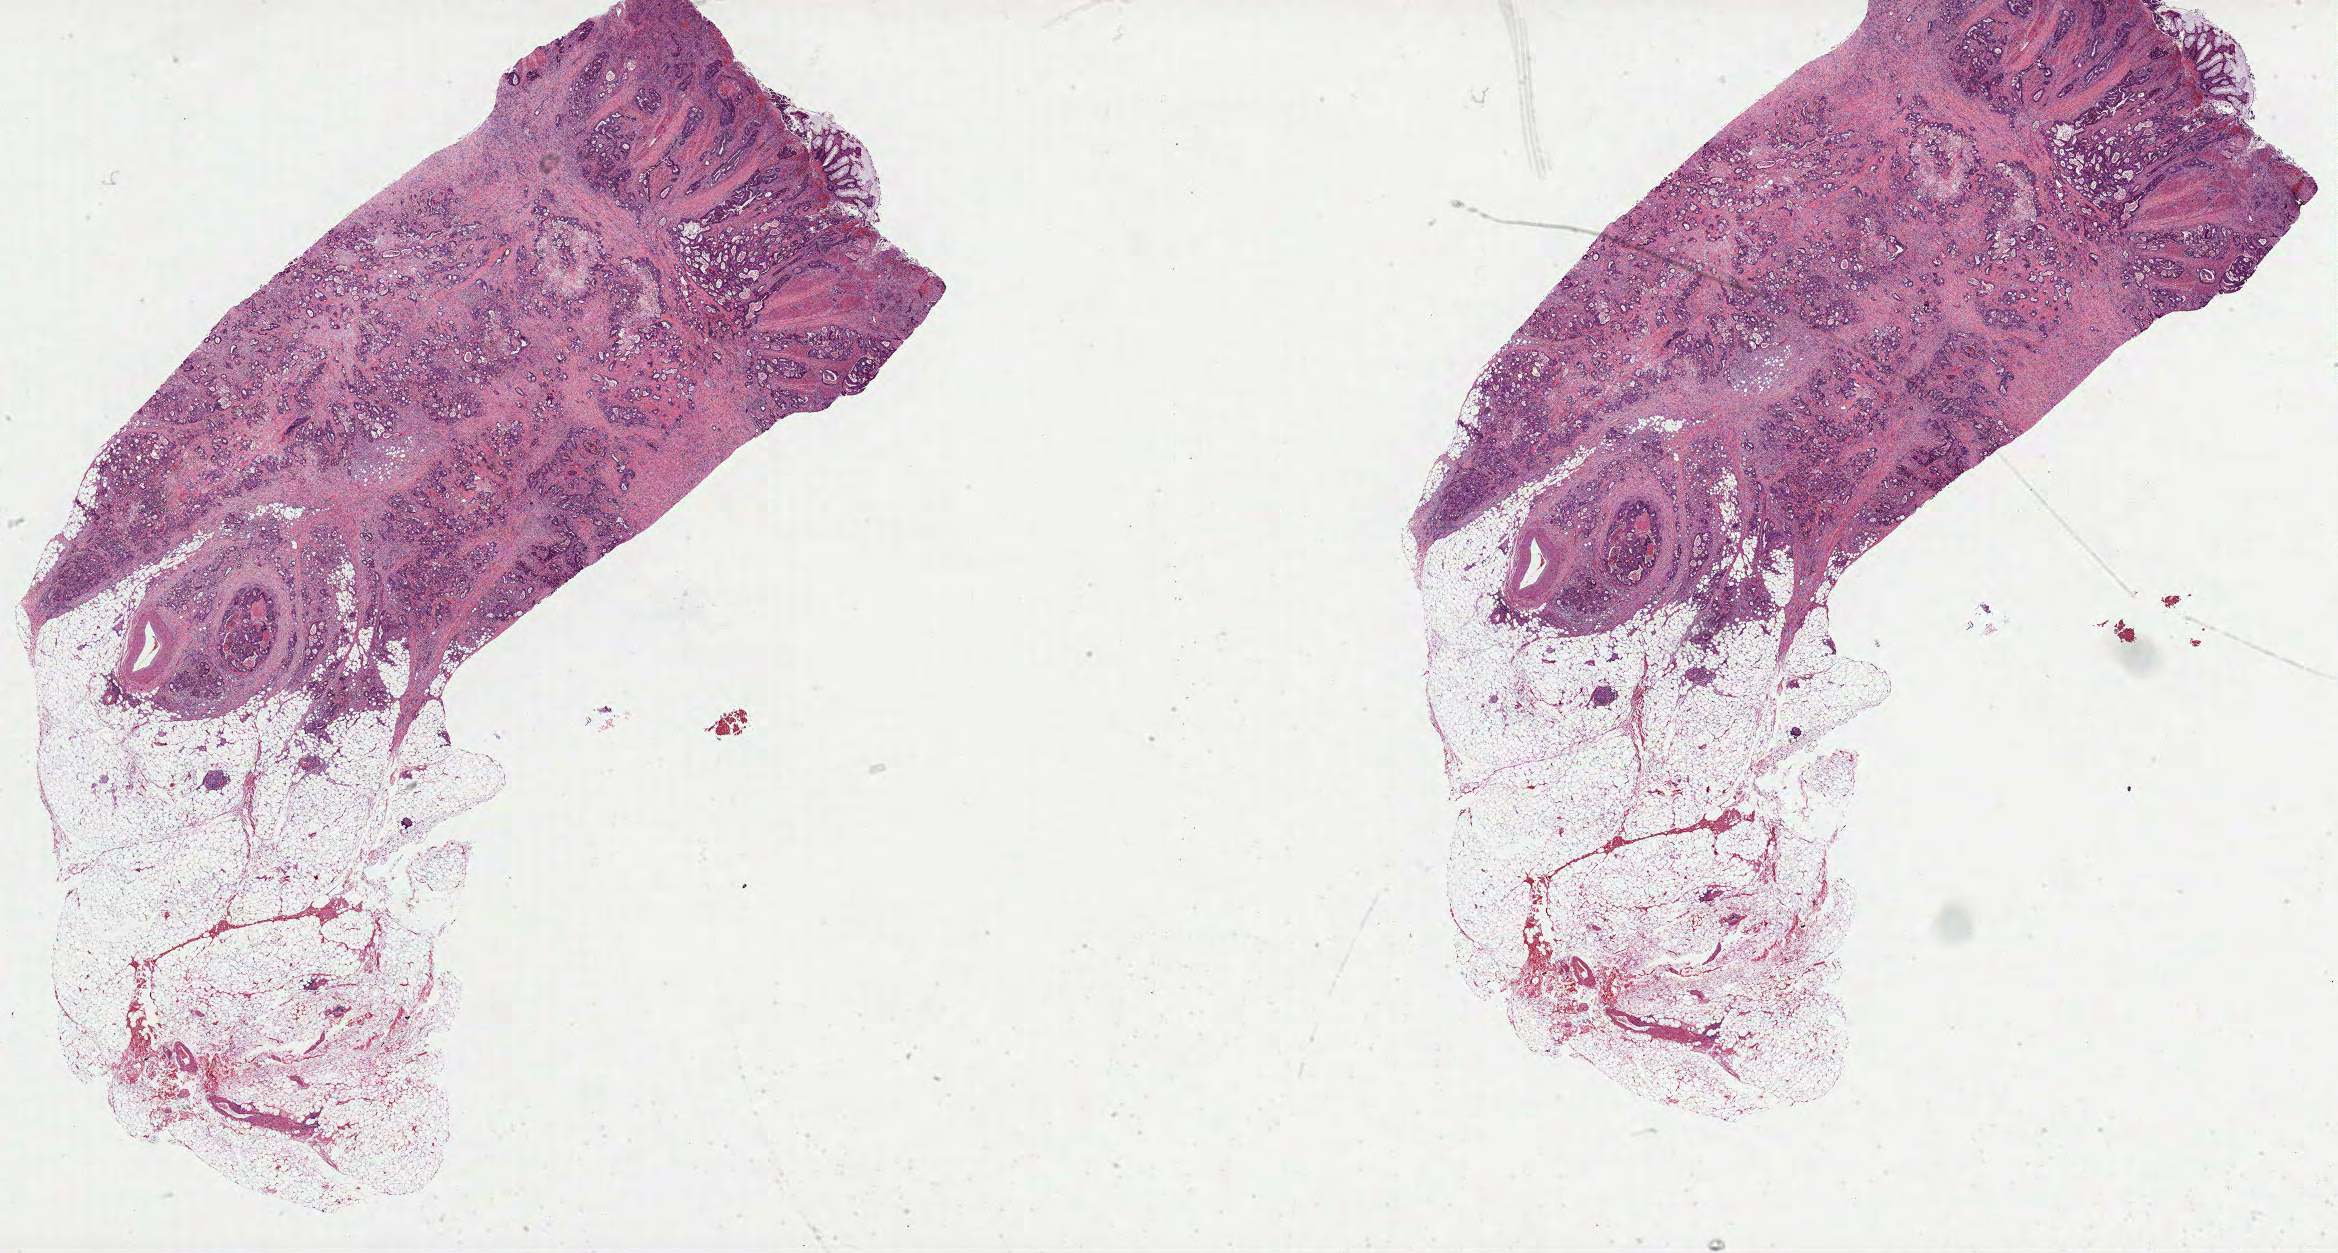
Digitized H&E tissue section (whole slide) — a low-resolution overview of the entire scanned area, about 37.7 x 20.2 mm, formalin-fixed paraffin-embedded (FFPE) diagnostic section, primary tumour sample from the rectum. Female patient; age at initial diagnosis 76 years.
* TNM: T3 N2 M0
* AJCC pathologic stage: IIIC
* histologic diagnosis: Adenocarcinoma, NOS